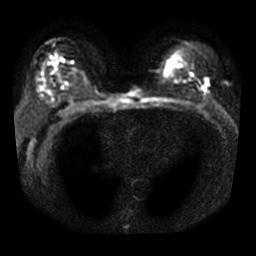
Breast MRI, one axial slice. Position 20 of 33 along the scan axis. Diffusion-weighted series; image 2 of 4 stored at this slice position (different b-values; order by instance number). 3 T. 5 mm slice thickness. 256 × 256 image matrix, field of view 320 × 320 mm. Female patient.
Structures marked on this image (manually delineated by an expert):
- tumour on diffusion-weighted imaging: bounding box <203,88,205,91> (left, top, right, bottom; pixels)